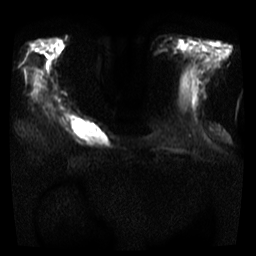
Breast MRI, one axial slice; position 10 of 35 along the scan axis; diffusion-weighted series; image 2 of 4 stored at this slice position (different b-values; order by instance number); 3 T; 5 mm slice thickness; 256 × 256 image matrix. Female patient.
Annotated regions visible in this slice (outlined manually by an expert reader):
- tumour on diffusion-weighted imaging: bounding box <69,119,109,145> (left, top, right, bottom; pixels)